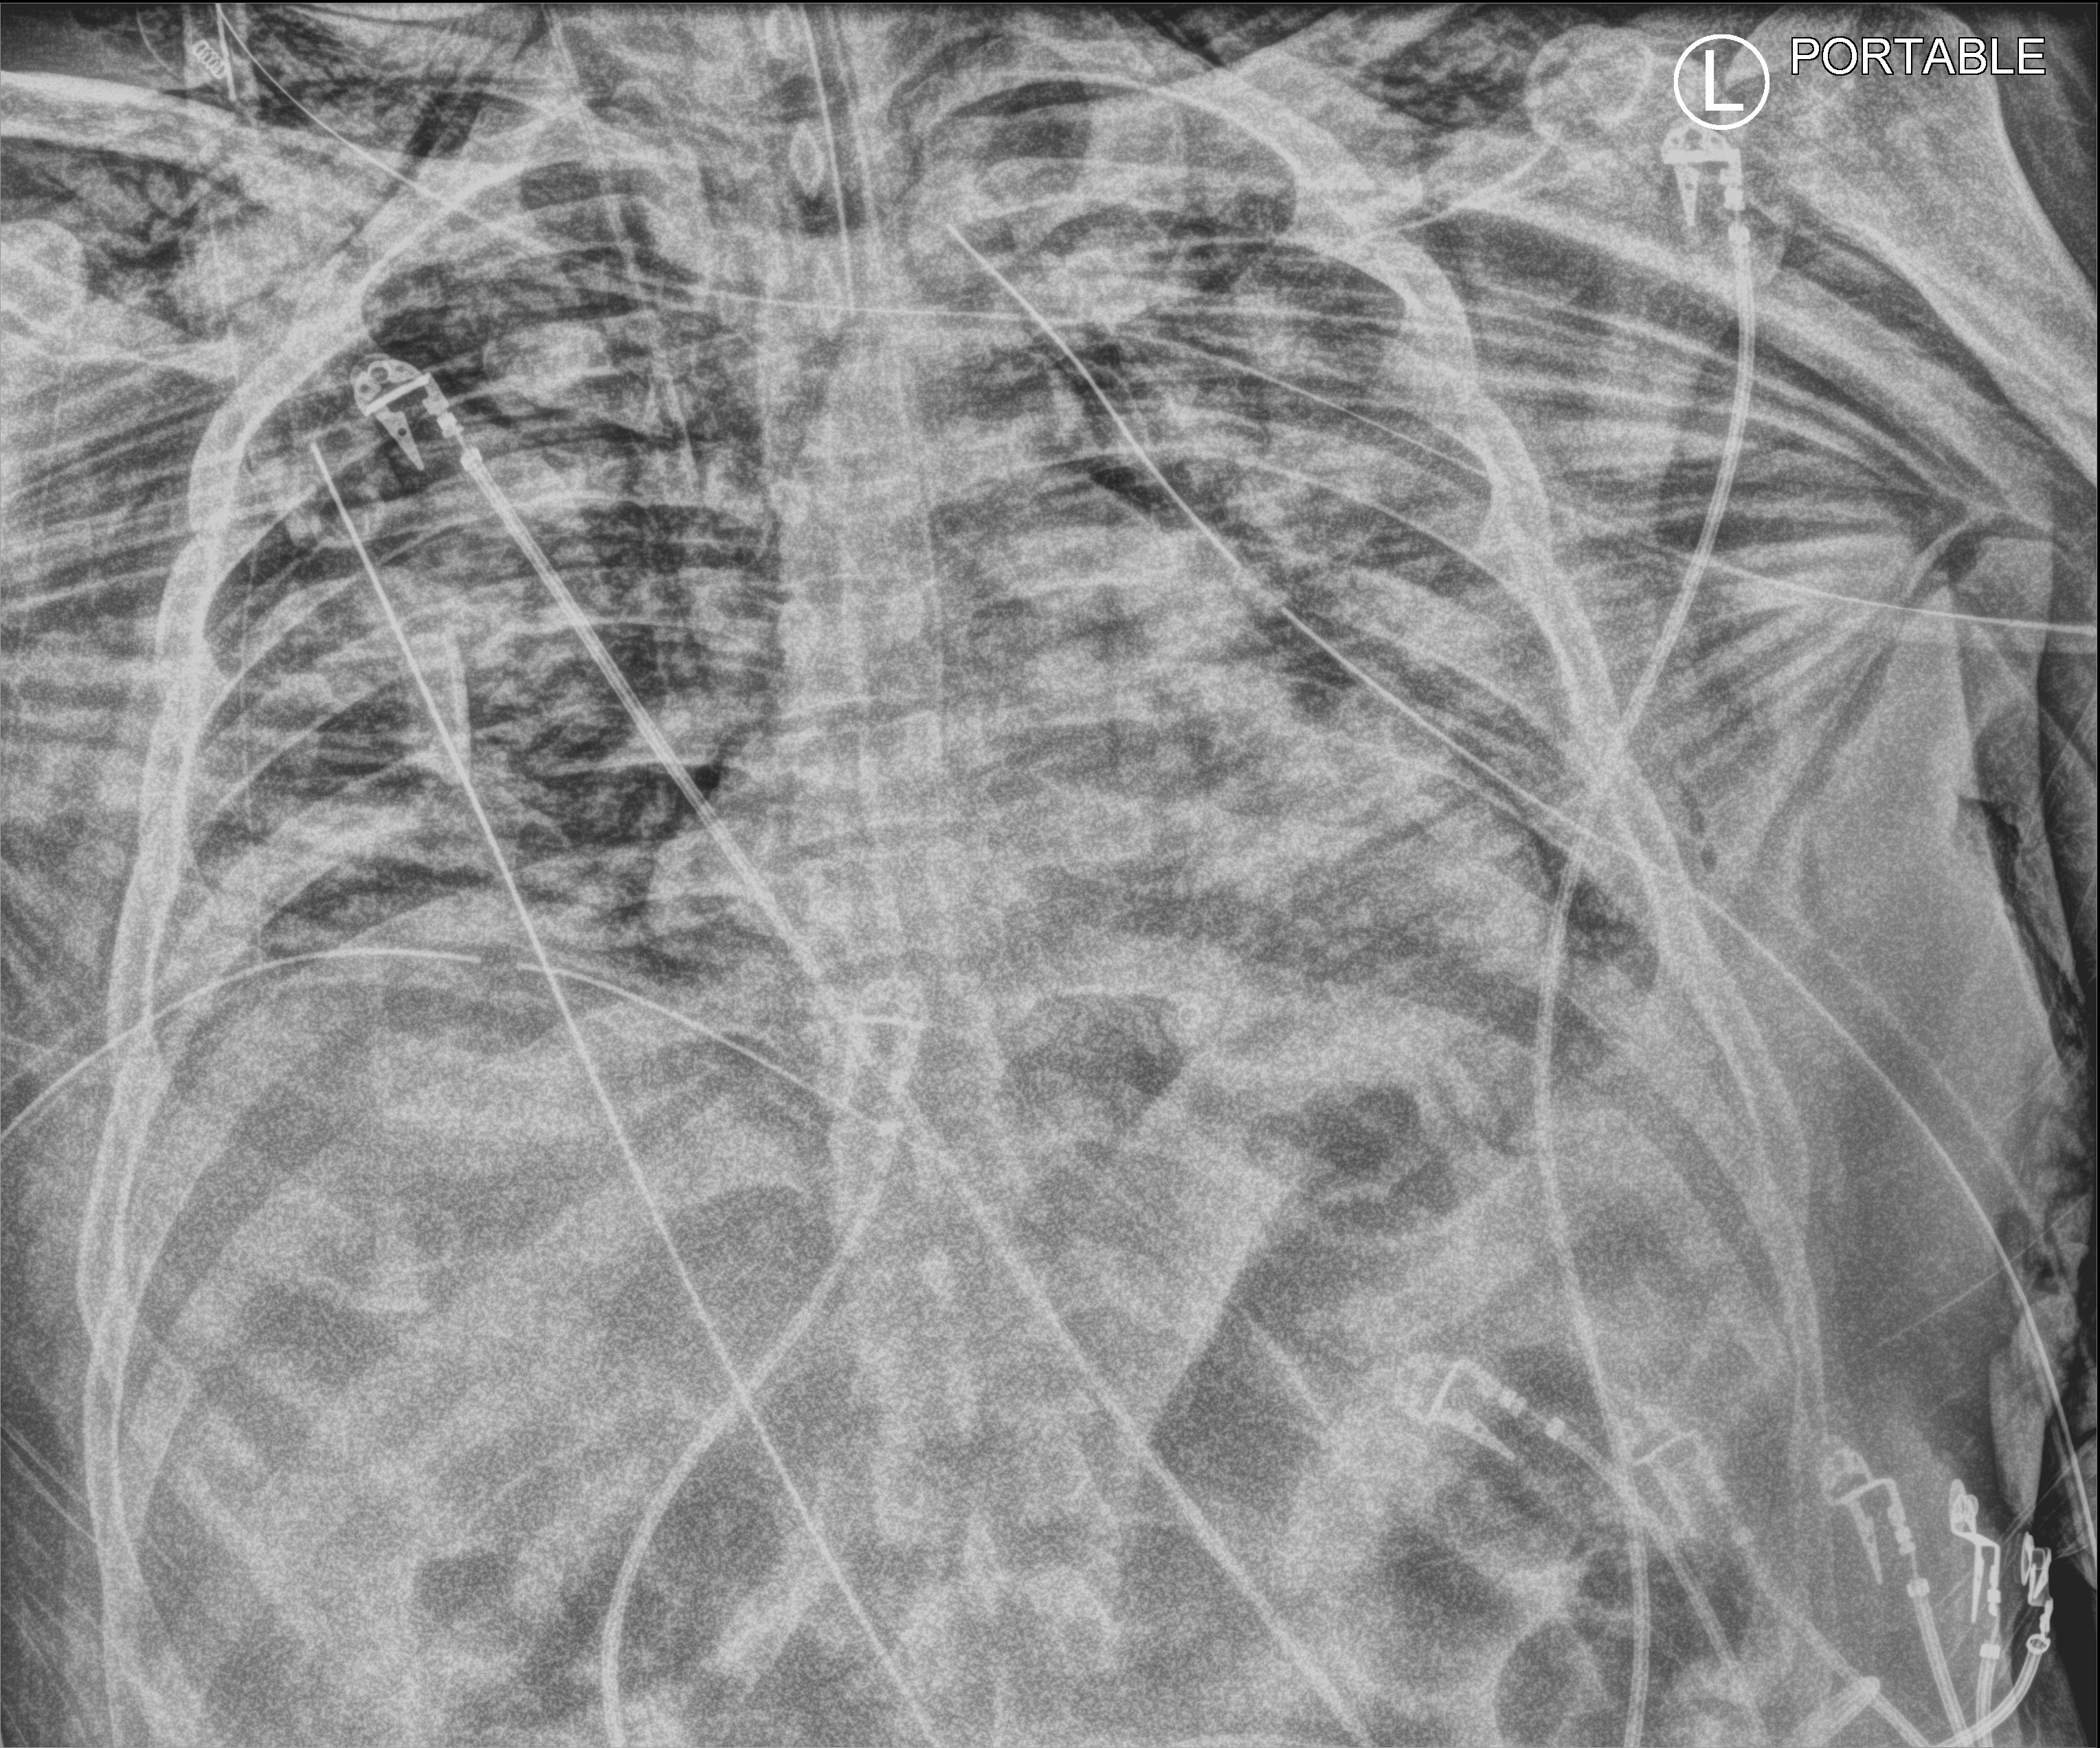
Chest X-ray (portable); anteroposterior (AP) projection. Patient hospitalised with COVID-19; male, aged 18–59 years.
Admission-level facts for this patient (not findings on this image; timing relative to this image not recorded):
- admitted to intensive care during this hospital stay: yes